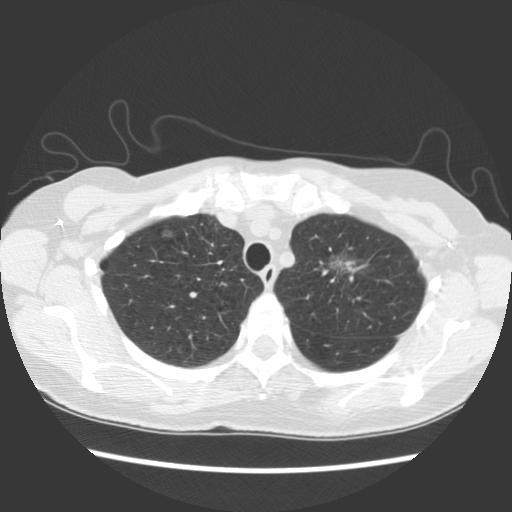
Low-dose screening chest CT, axial slice; baseline screening round; lung window (W 1500 / L -600 HU); 2.5 mm slice thickness; 512 × 512 image matrix, field of view 325 × 325 mm. Female participant, aged 65 years at enrolment. Former smoker at enrolment.
Expert reader's lesion annotation, bounding box [x1, y1, x2, y2] px = [312, 238, 380, 297]. Screening reader's record for this exam (one nodule recorded; not confirmed to be the boxed lesion): non-calcified nodule or mass ≥4 mm, left upper lobe, 11 × 10 mm, poorly defined margins, ground glass attenuation. Official screen result: positive, change unspecified: nodule(s) >= 4 mm or enlarging nodule(s), mass(es), or other non-specific abnormalities suspicious for lung cancer.